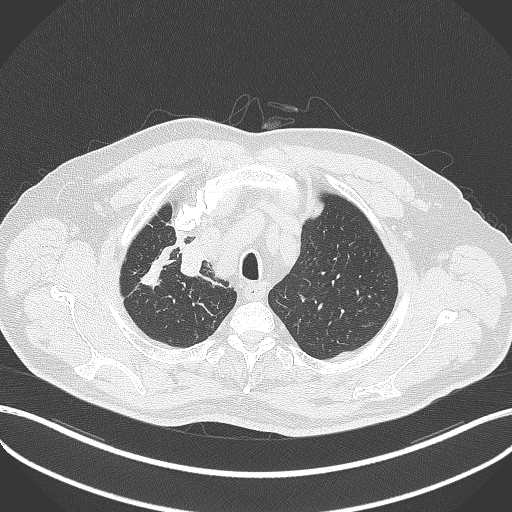
Chest CT, one axial slice; position 324 of 411 along the scan axis; reconstruction kernel B70f; 120 kVp; lung window (W 1500 / L -600 HU); 512 × 512 image matrix, field of view 400 × 400 mm. Patient: male, 60 years. From the clinical record (not read from this slice): clinical TNM (as recorded): T1b N1 M0.
Outlined on this slice (bounding box drawn by a radiologist):
- lung tumour (recorded histology: squamous cell carcinoma): bounding box <180,237,212,282> (left, top, right, bottom; pixels)